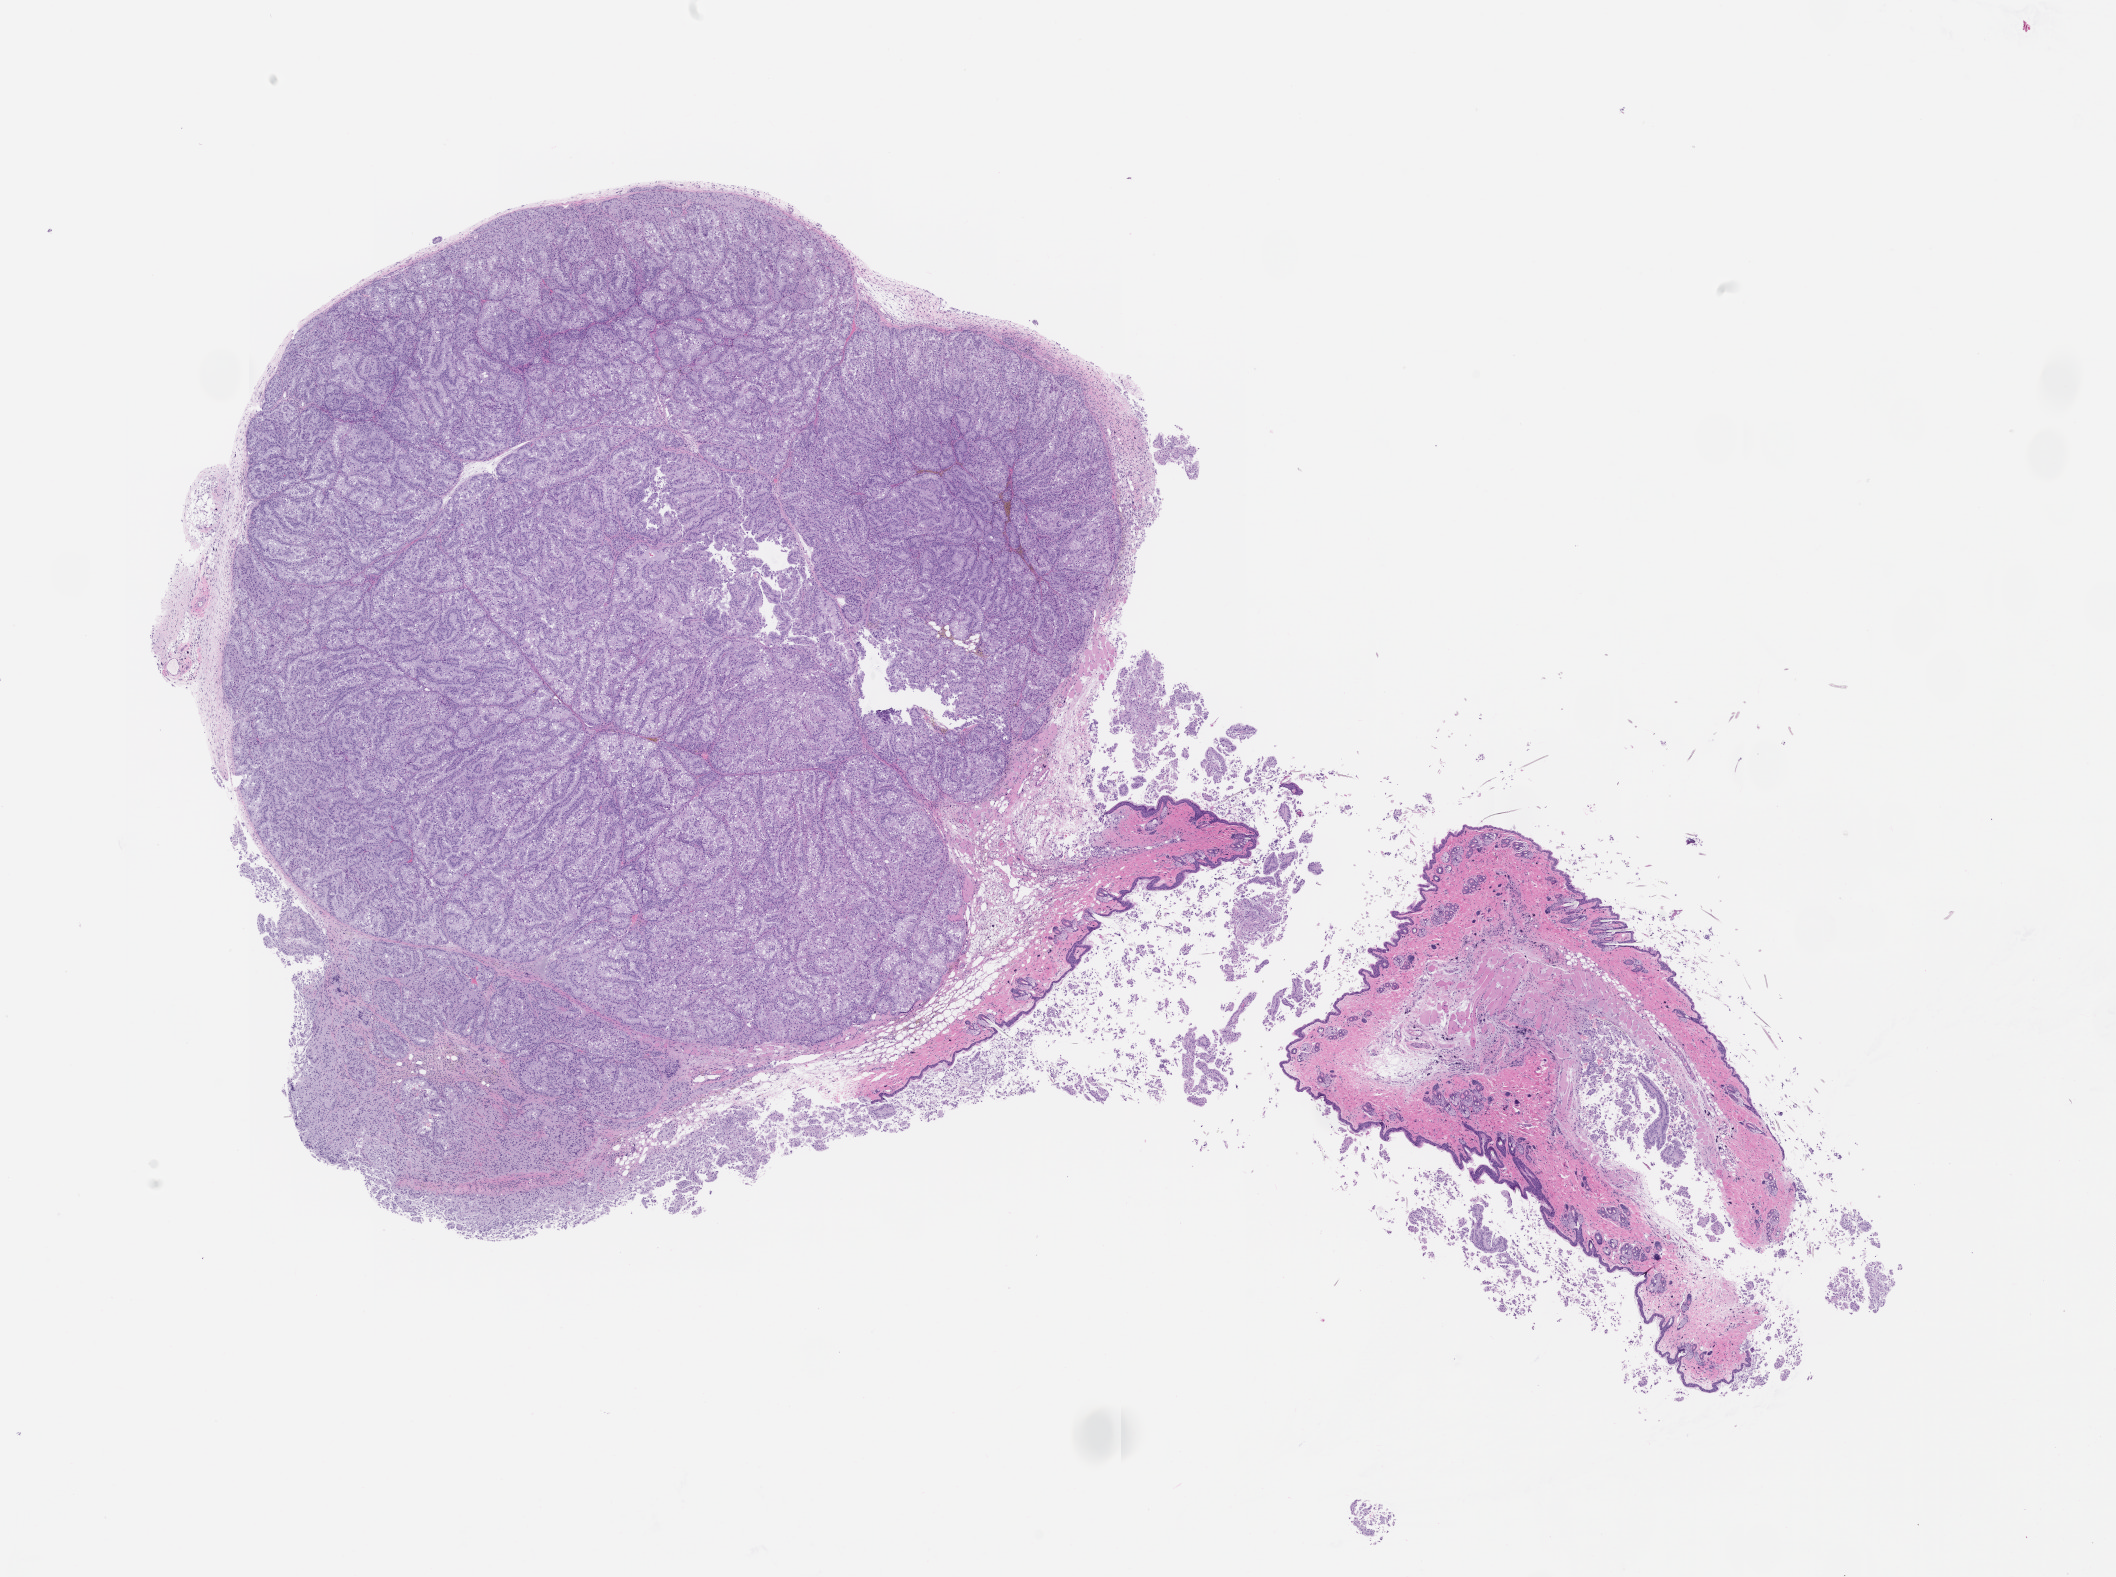
Hematoxylin and eosin (H&E) whole-slide image of a patient-derived xenograft (PDX) tumor grown in a mouse, passage 2, a low-resolution overview of the entire scanned area, about 17.0 x 12.6 mm, formalin-fixed paraffin-embedded section, tumor site category: genitourinary tract.
Originating patient diagnosis: Renal Cell Carcinoma, Not Otherwise Specified.